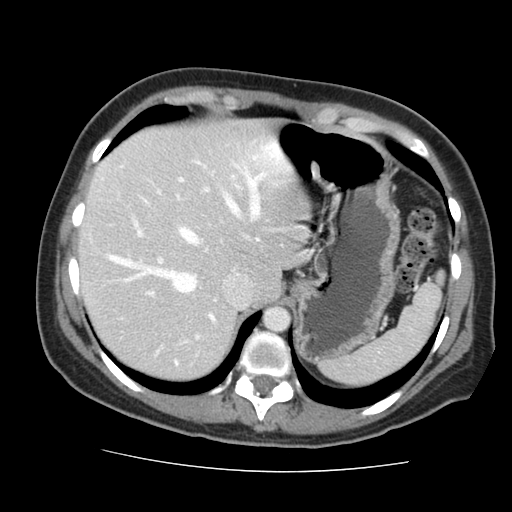
Contrast-enhanced abdominal CT, one axial slice. 120 kVp. Soft-tissue window (W 400 / L 40 HU). 512 × 512 image matrix. Female patient, age 46 years. Case-level facts recorded for this patient, not image findings: diagnosis: colorectal cancer liver metastases, imaged before liver resection; multiple liver metastases: no; largest metastasis: 2.8 cm; chemotherapy before resection: yes.
Outlined on this slice (manually delineated by an expert):
- hepatic veins: bounding box [x1, y1, x2, y2] px = [109, 173, 264, 293]
- liver: [81, 122, 306, 379]
- planned liver remnant (the part of the liver to remain after resection): [81, 122, 306, 379]
- portal vein (with intrahepatic branches): [107, 175, 240, 365]